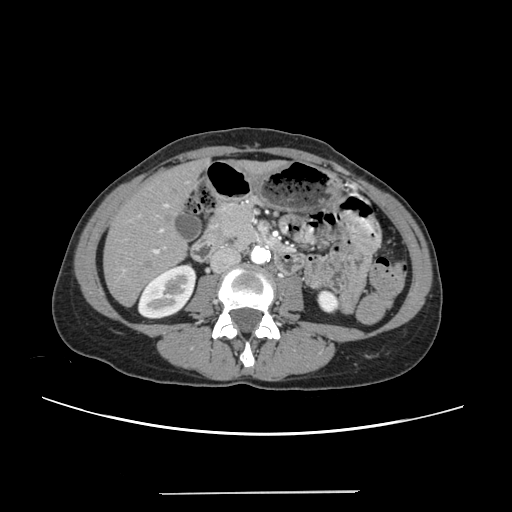
Contrast-enhanced abdominal CT, one axial slice. Slice 83 of 240 in the series (ordered by position). Intravenous contrast given. Soft-tissue window (W 400 / L 40 HU). 512 × 512 image matrix, field of view 371 × 371 mm. Female patient, age 60 years. Case-level facts recorded for this patient, not image findings: diagnosis: colorectal cancer liver metastases, imaged before liver resection; multiple liver metastases: no; largest metastasis: 1.5 cm.
Outlined on this slice (expert manual segmentation):
- liver: bounding box <105,163,201,305> (left, top, right, bottom; pixels)
- planned liver remnant (the part of the liver to remain after resection): <105,172,187,304>
- portal vein (with intrahepatic branches): <123,204,168,270>